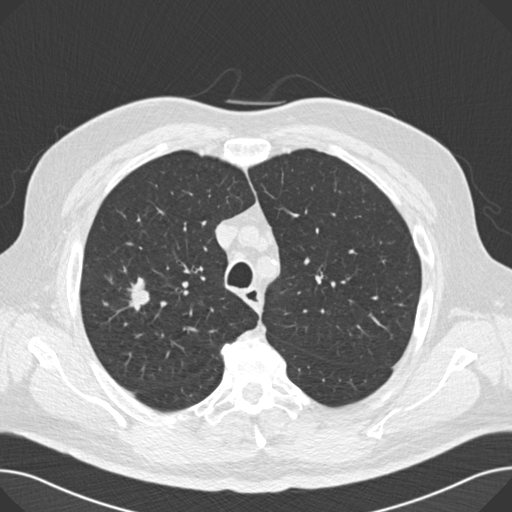
Axial slice from a low-dose chest CT screening exam. Second annual screen. Lung window (W 1500 / L -600 HU). 2 mm slice thickness. Male participant, aged 67 years at enrolment. Current smoker at enrolment.
• Expert-annotated lung lesion, bounding box <123,279,158,312> (left, top, right, bottom; pixels).
• No non-calcified nodule or mass ≥4 mm was recorded by the screening reader at this exam.
• Participant outcome: lung cancer diagnosed 194 days after this screen — small cell carcinoma, NOS, right middle lobe, stage IA (AJCC 6th edition), 20 mm at pathology.